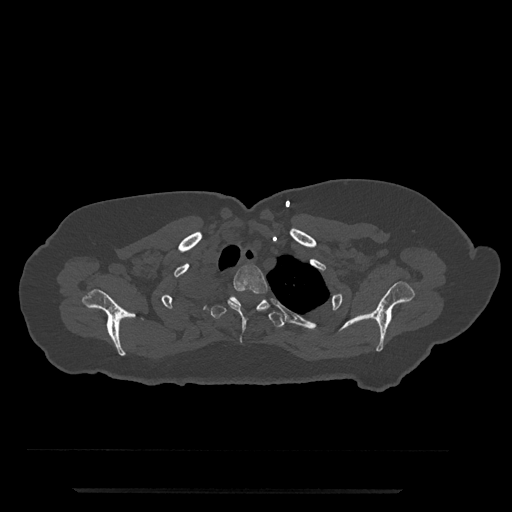
CT including the spine, one axial slice; position 658 of 797 along the scan axis; 120 kVp; bone window (W 1800 / L 400 HU); 512 × 512 image matrix, field of view 440 × 440 mm. Female patient, age 51 years. From the clinical record (not read from this slice): primary cancer: neuro.
Annotated regions visible in this slice (semi-automatically segmented with operator editing):
- T2 vertebra: bounding box <227,265,268,331> (left, top, right, bottom; pixels)
- T3 vertebra: <211,295,284,328>